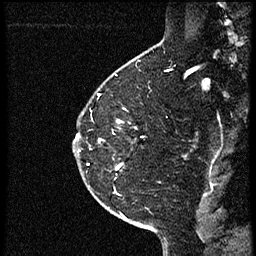
Breast MRI (dynamic contrast-enhanced), one sagittal slice. Slice 43 of 56 in the series (ordered by position). Dynamic contrast-enhanced study with each time point stored as its own series, time point 2 of 4 at this slice position (early post-contrast, ordered by acquisition time). 1.5 T. TE 4.2 ms, TR 18.9 ms. 2 mm slice thickness. 256 × 256 image matrix, field of view 200 × 200 mm. Female patient. From the clinical record (not read from this slice): setting: breast cancer imaged before/during neoadjuvant chemotherapy; receptor status: HER2-positive.
Outlined on this slice (semi-automatically segmented with operator editing):
- analysis volume of interest (the breast-tissue region the enhancement analysis was run in; not a lesion): bounding box <78,108,148,189> (left, top, right, bottom; pixels)
- tumour enhancement mask (voxels above the 100 % enhancement threshold inside the analysis volume of interest): <89,163,120,169>